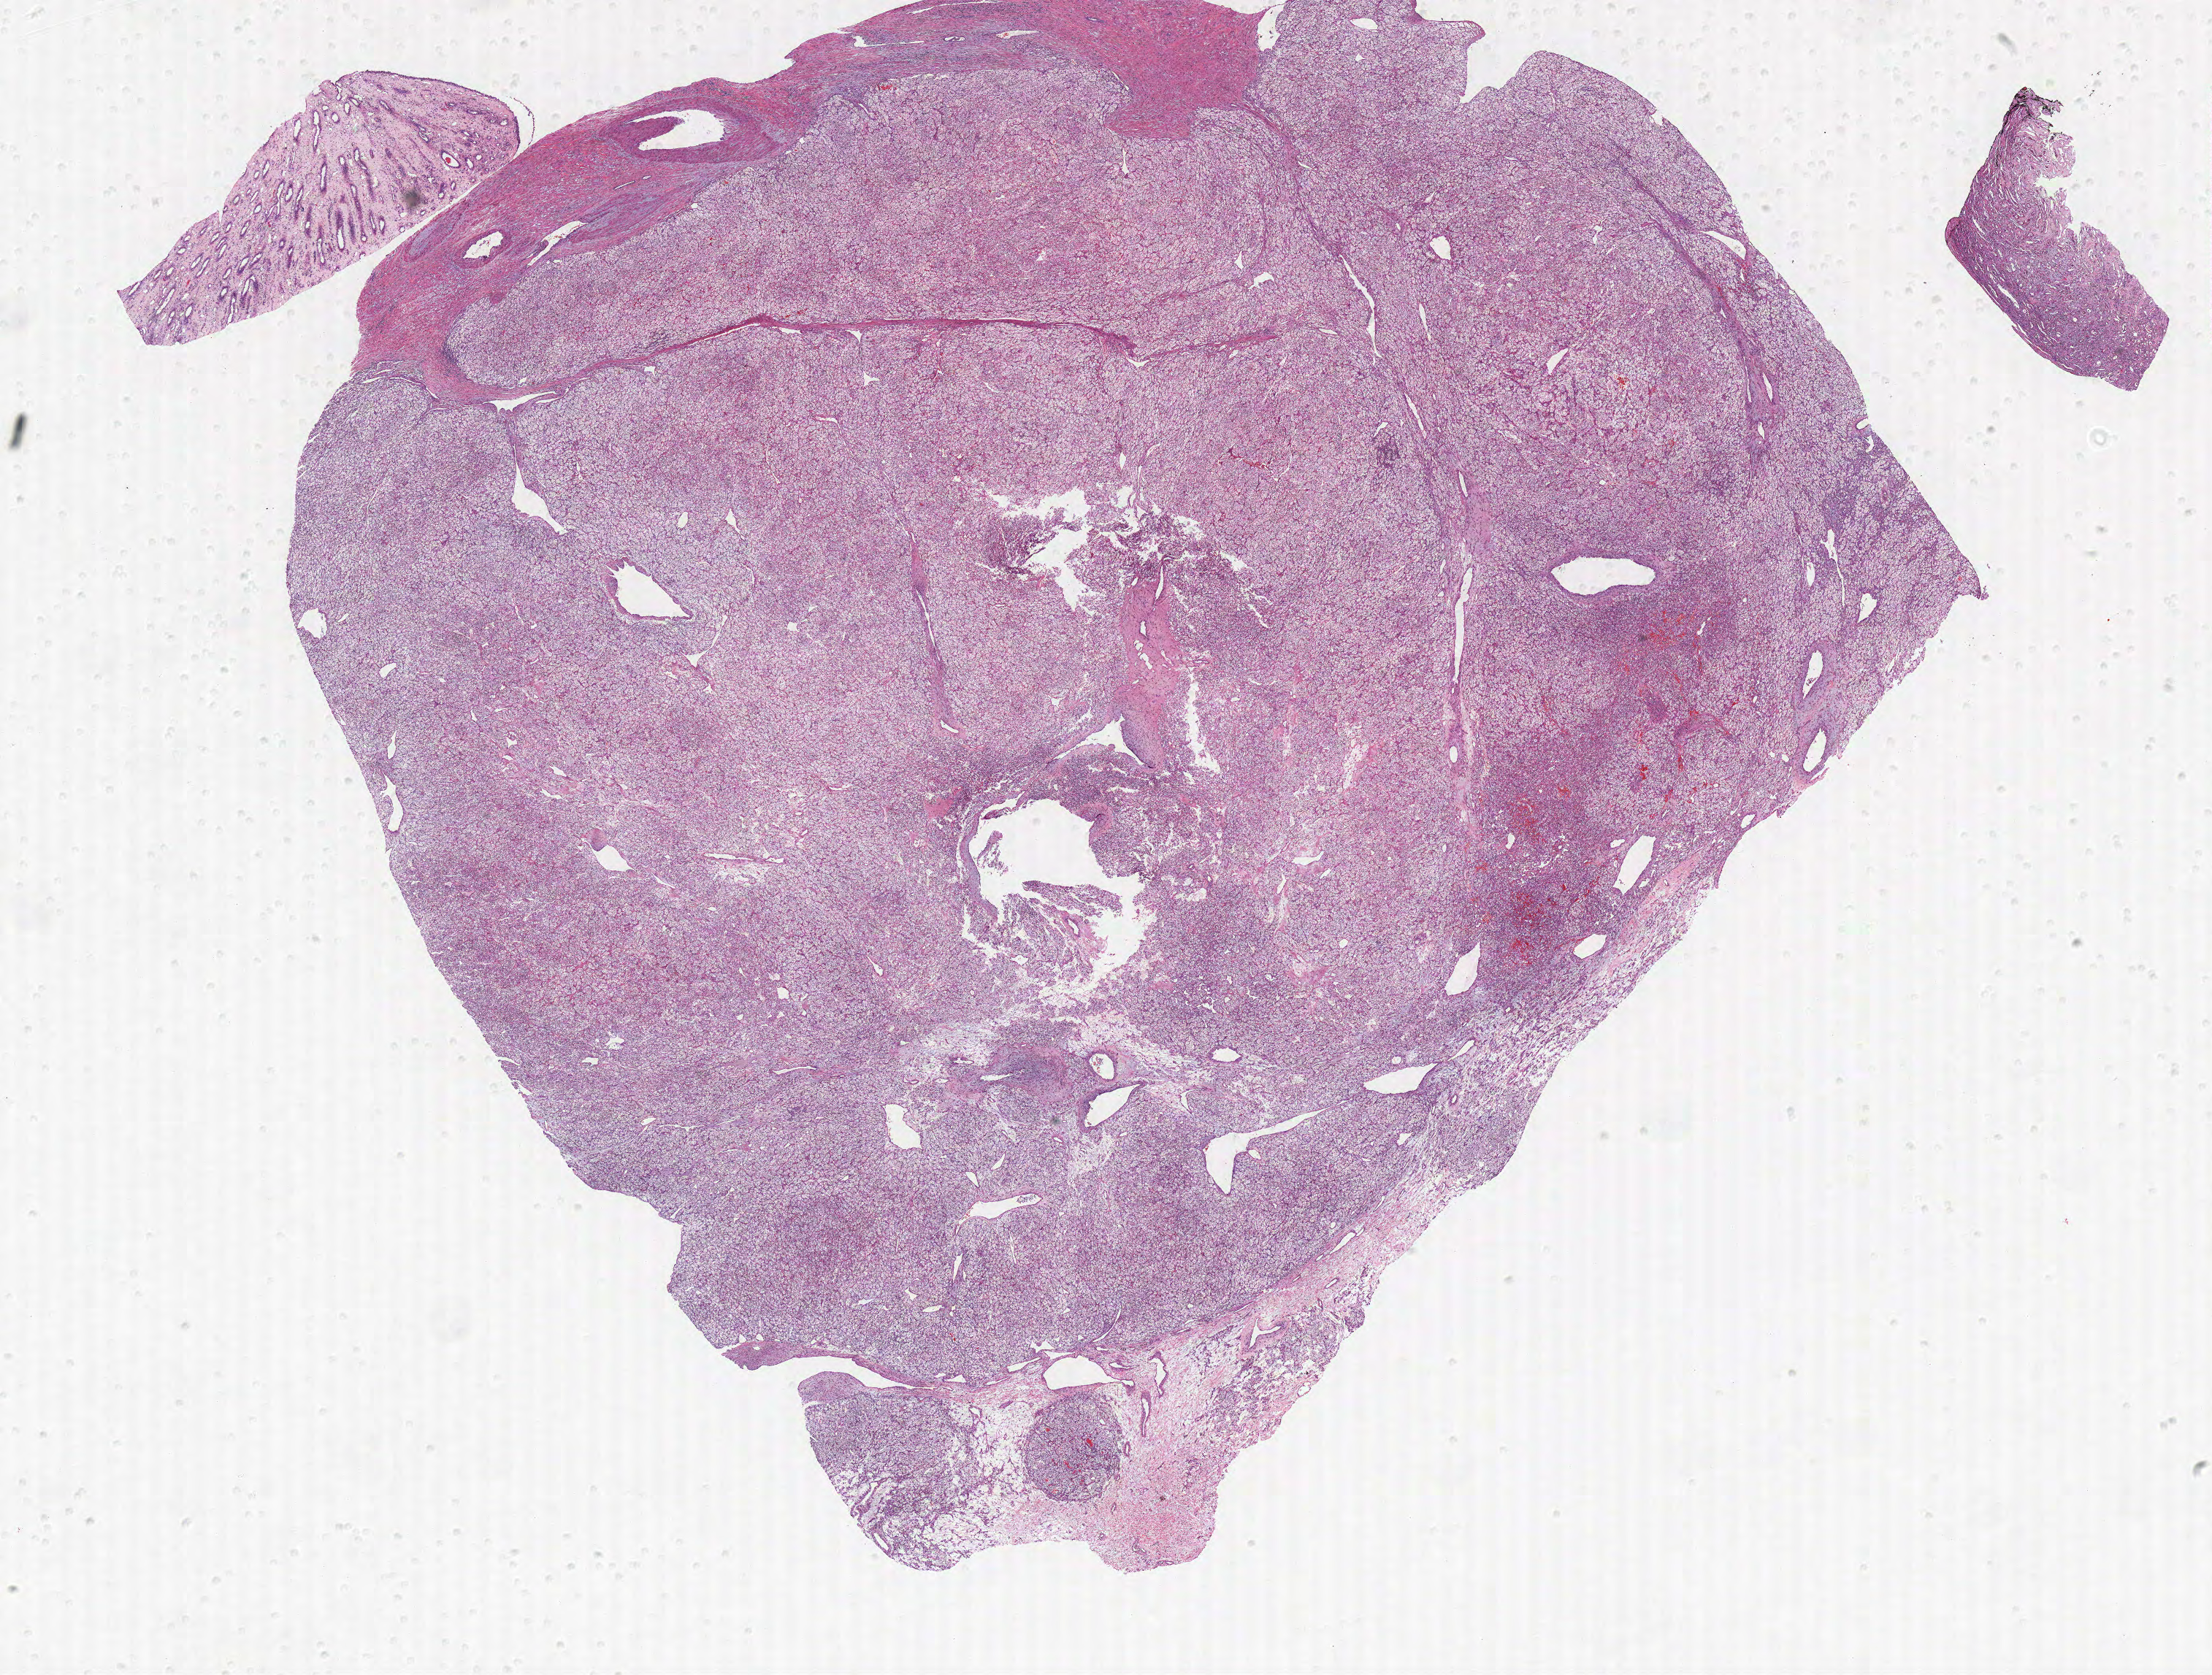
Digitized Hematoxylin and eosin (H&E) stained tissue section (whole slide), low-resolution overview of the scanned area, about 24.2 x 18.3 mm (from a 40x scan); formalin-fixed paraffin-embedded (FFPE) diagnostic section; sample: primary tumour, kidney. Patient: female, age at initial diagnosis 58 years. Histologic grade: G2 (moderately differentiated).
Pathologic diagnosis: Clear cell adenocarcinoma, NOS. AJCC pathologic stage: I.